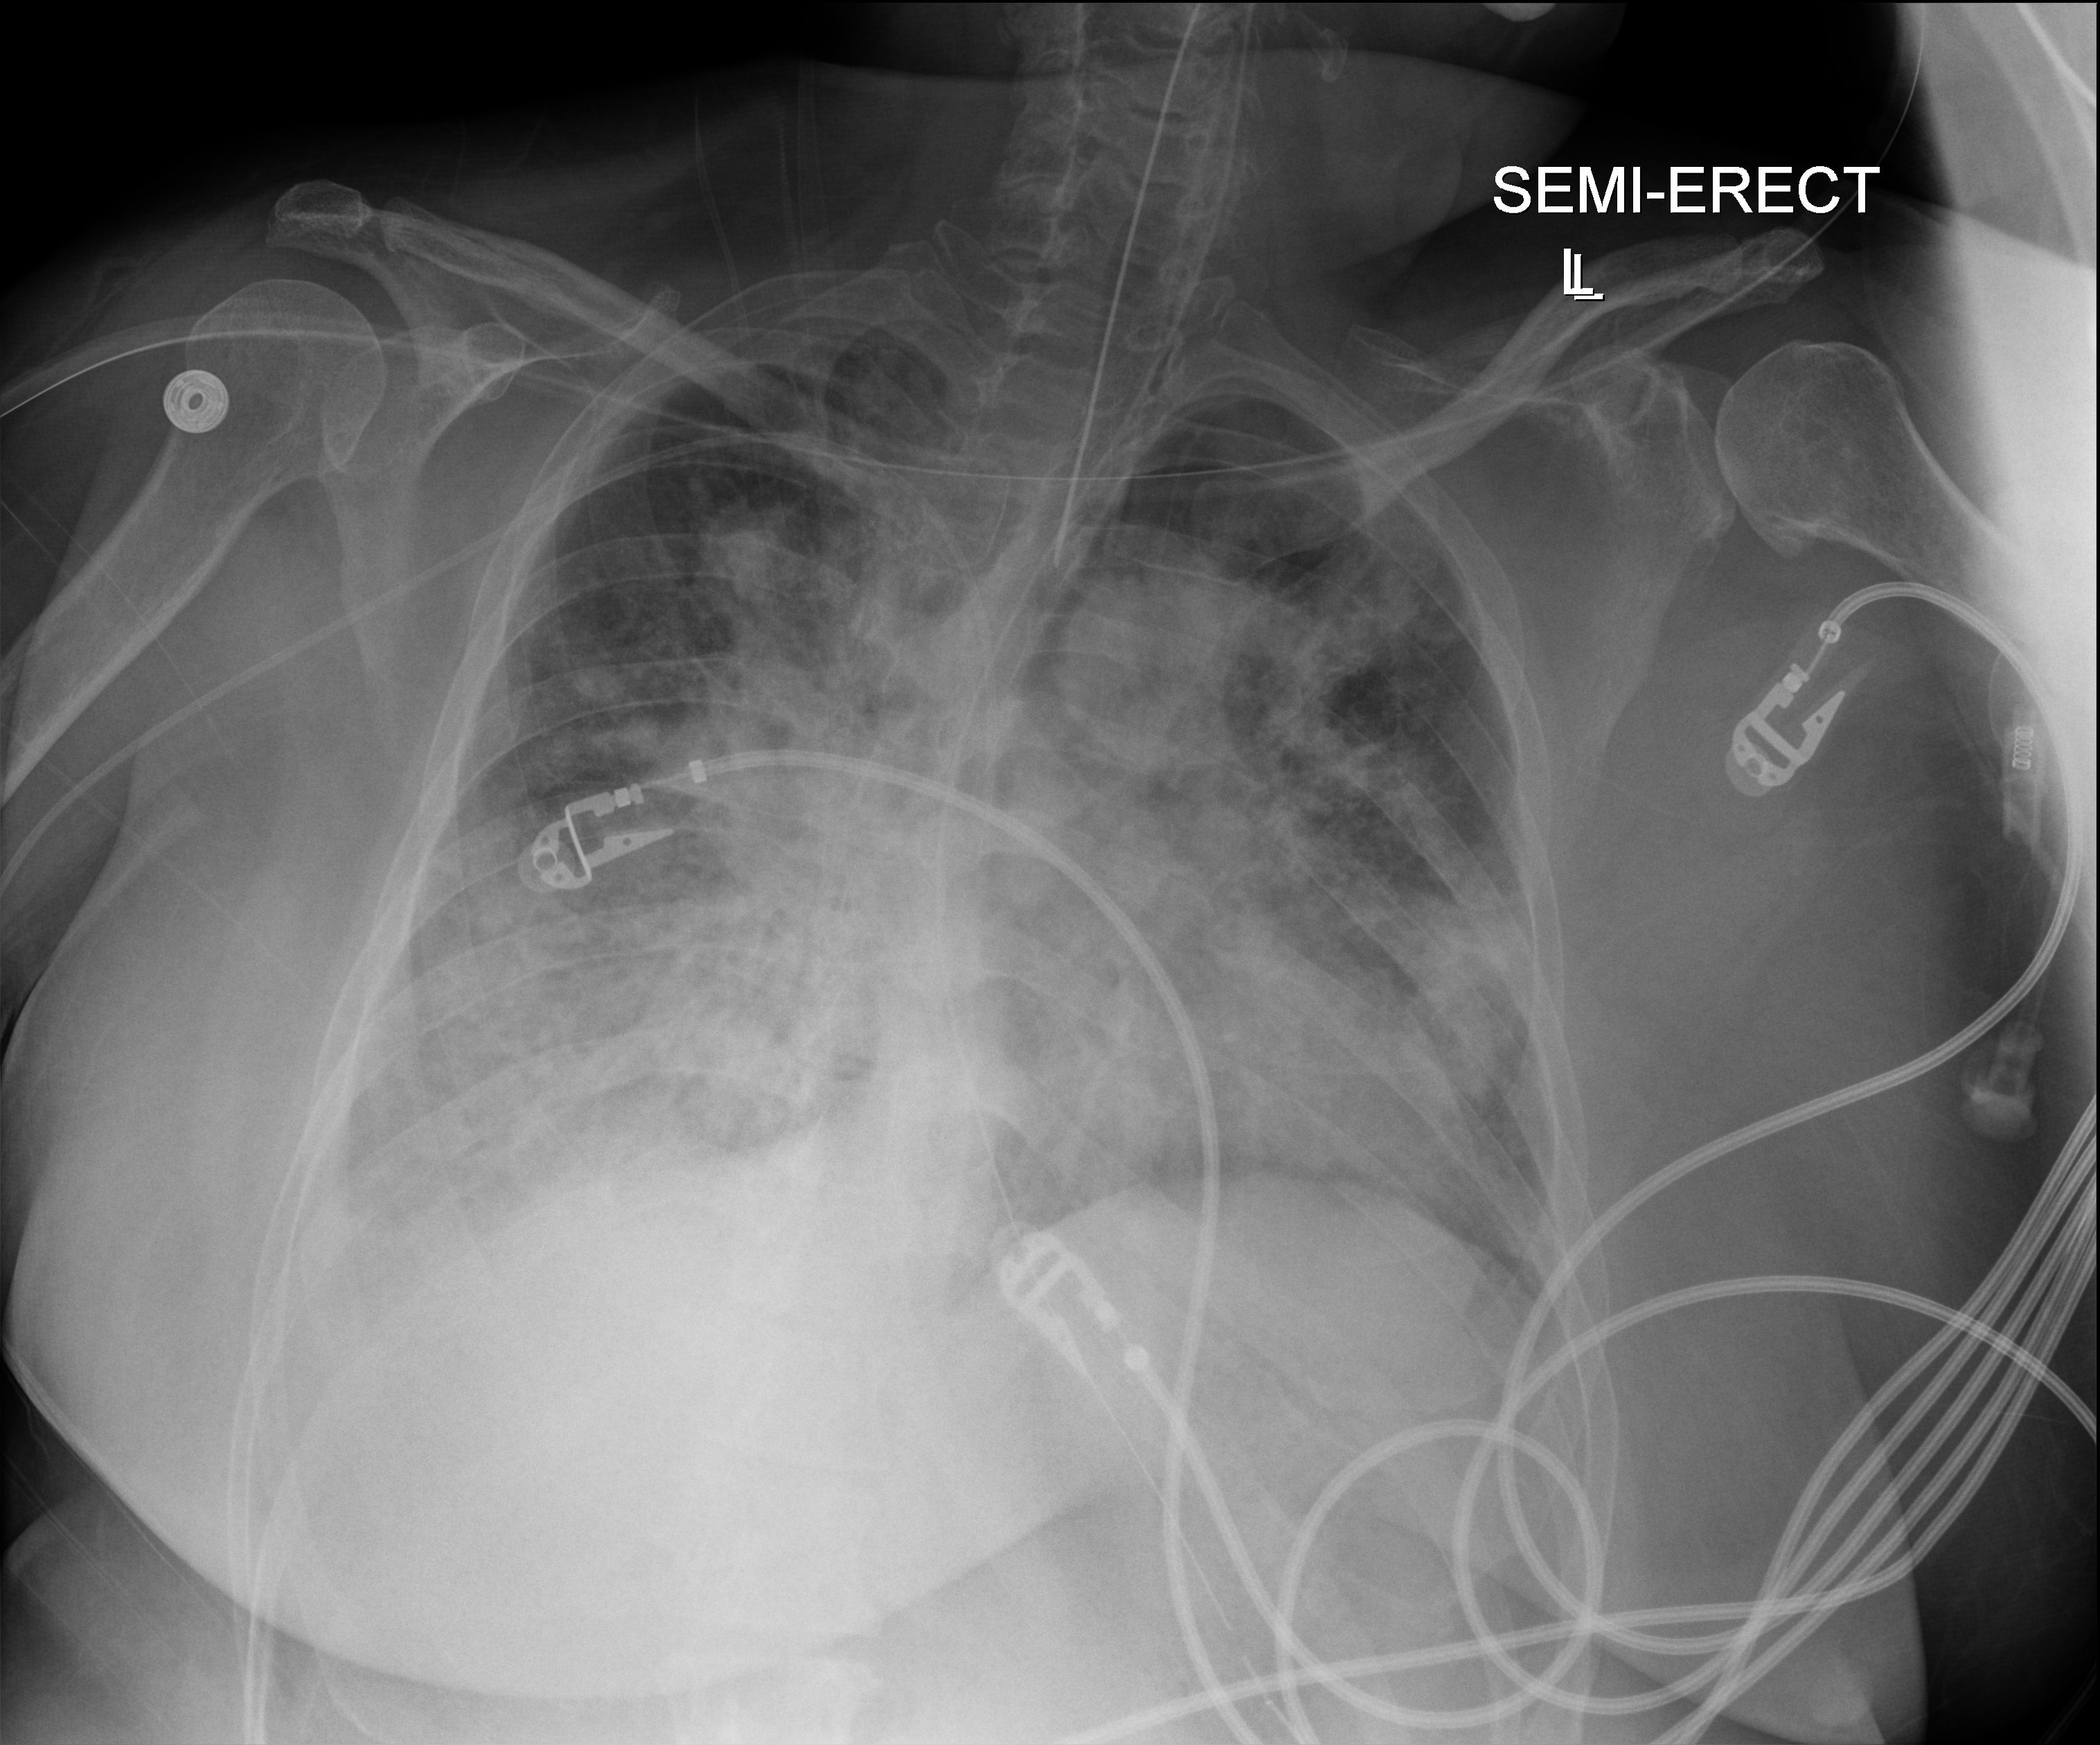
Chest X-ray (portable). Patient hospitalised with COVID-19, aged 18–59 years.
Admission-level facts for this patient (not findings on this image; timing relative to this image not recorded): length of hospital stay: 15 days; admitted to intensive care during this hospital stay: yes.